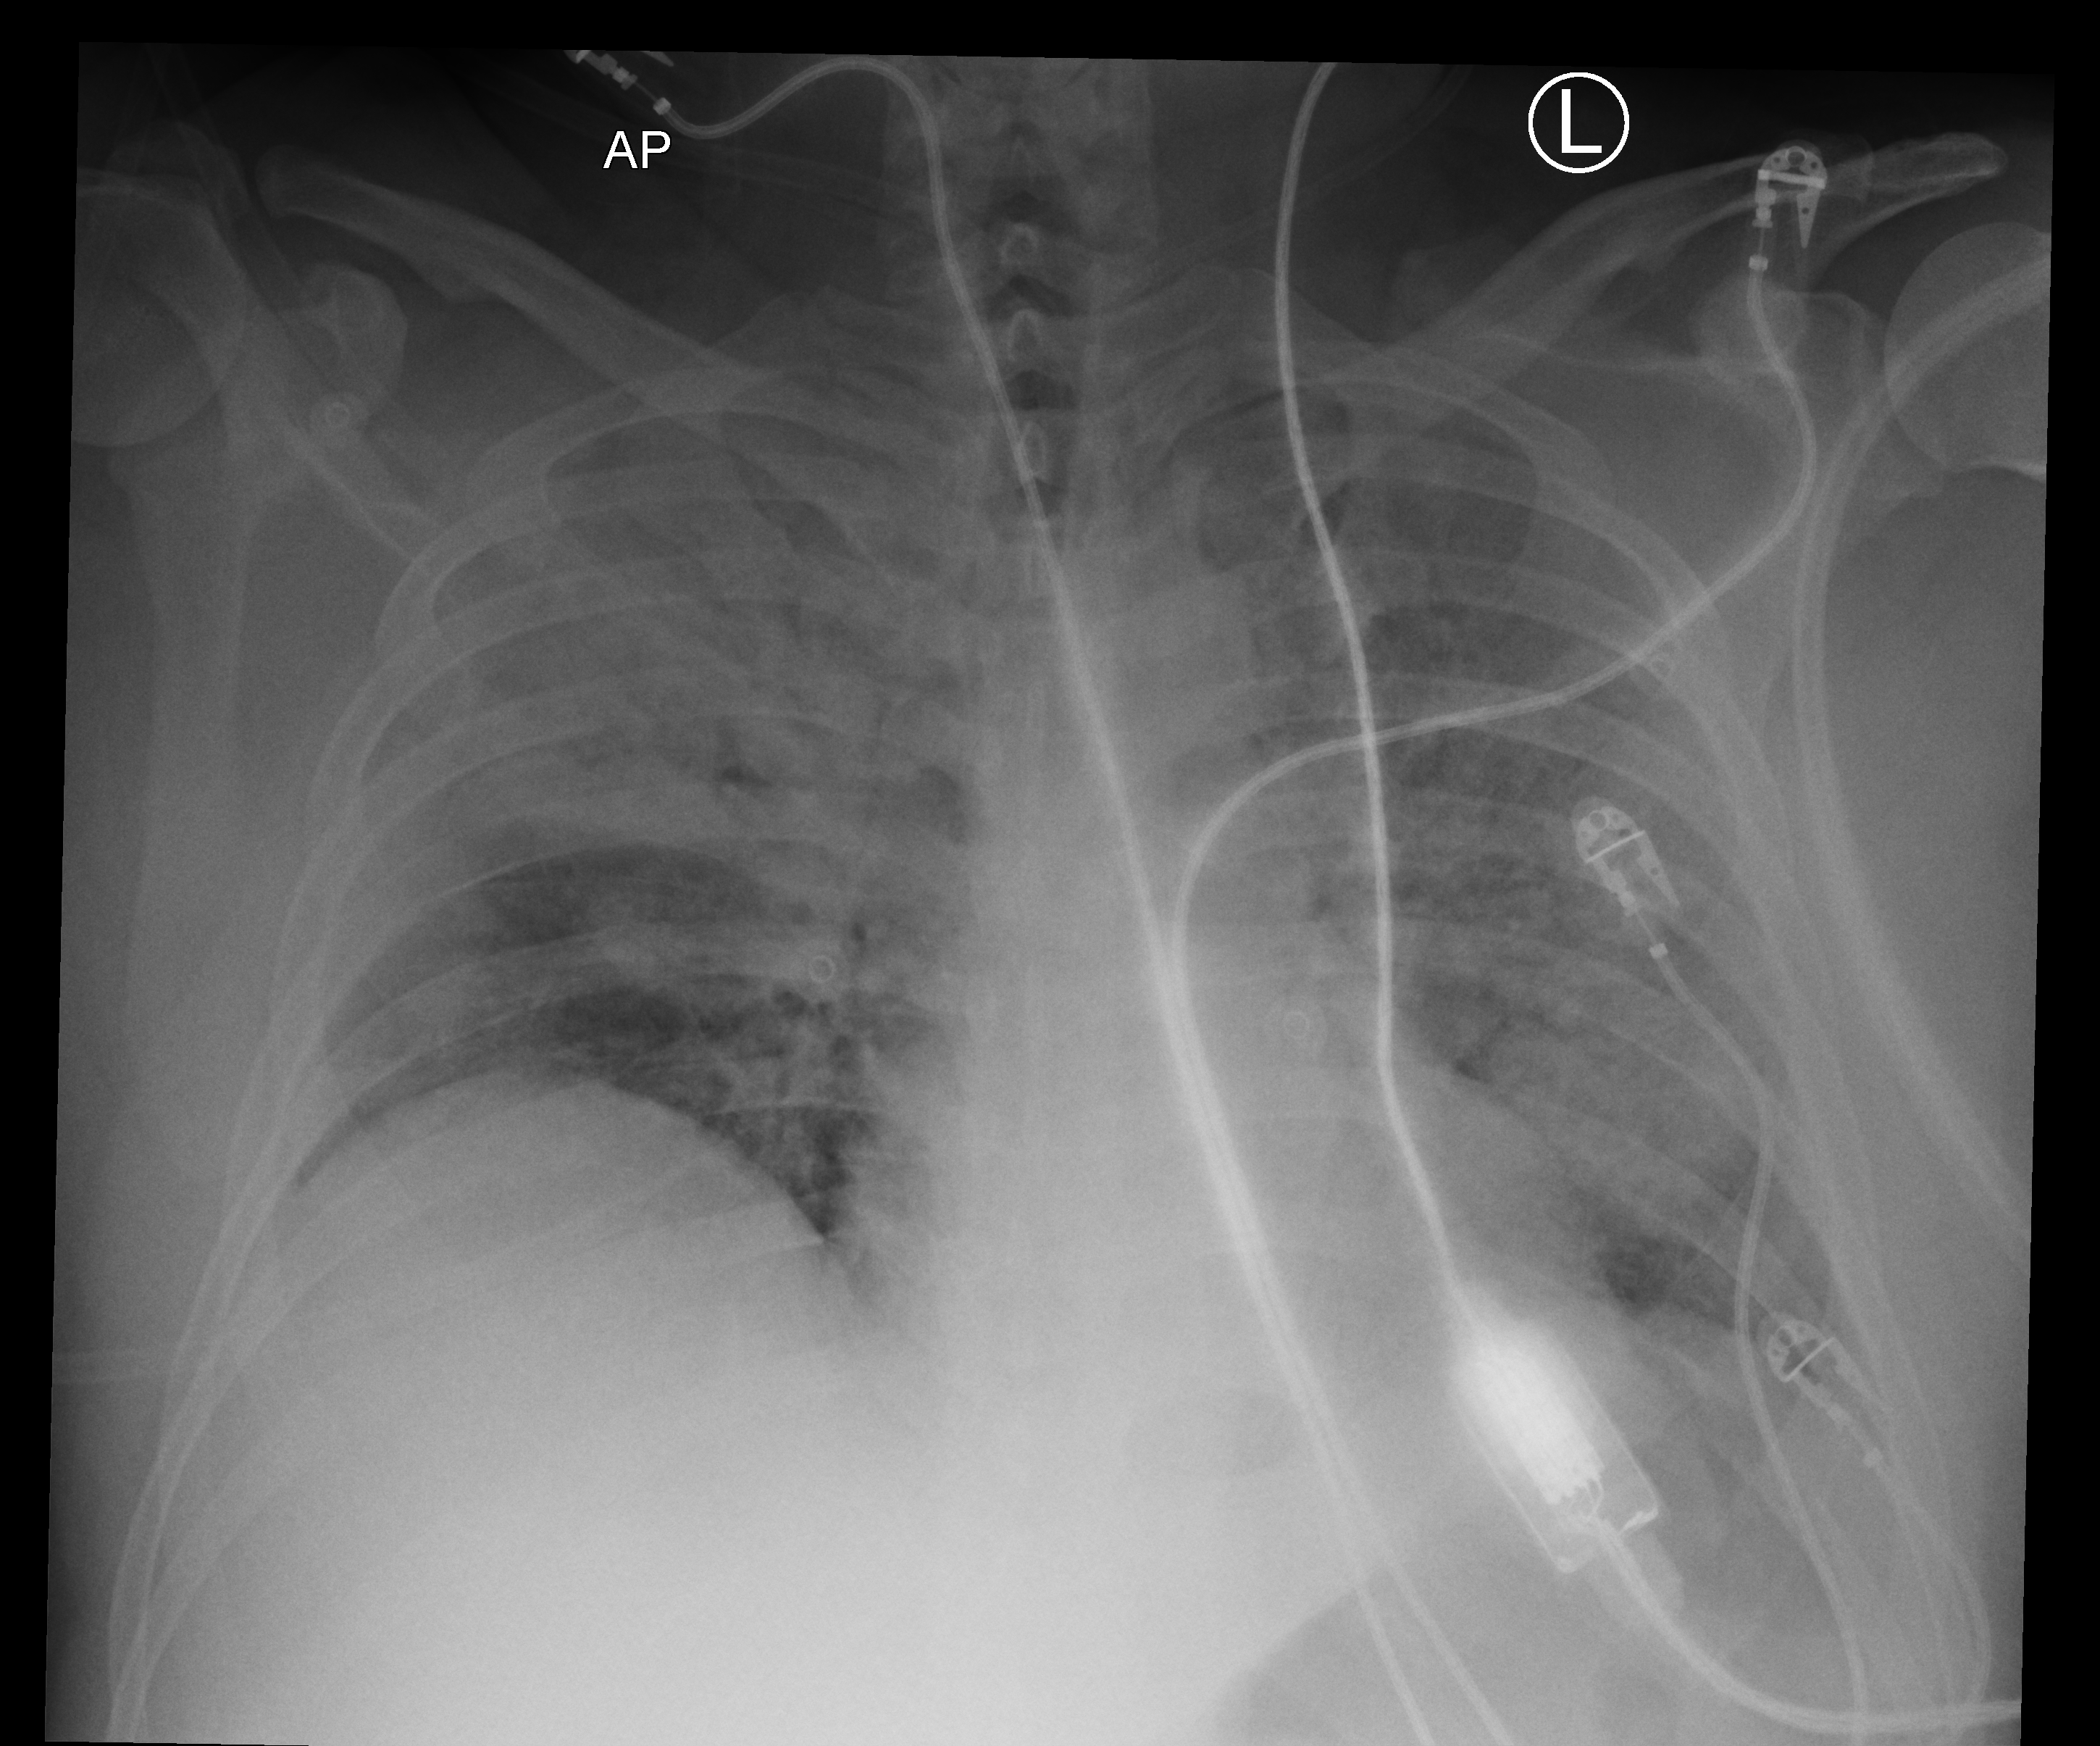
Portable chest radiograph. Male patient hospitalised with COVID-19, age 18–59 years.
Hospital-stay facts (about this admission, not read from this image; timing relative to this image not recorded):
- admitted to intensive care during this hospital stay: yes